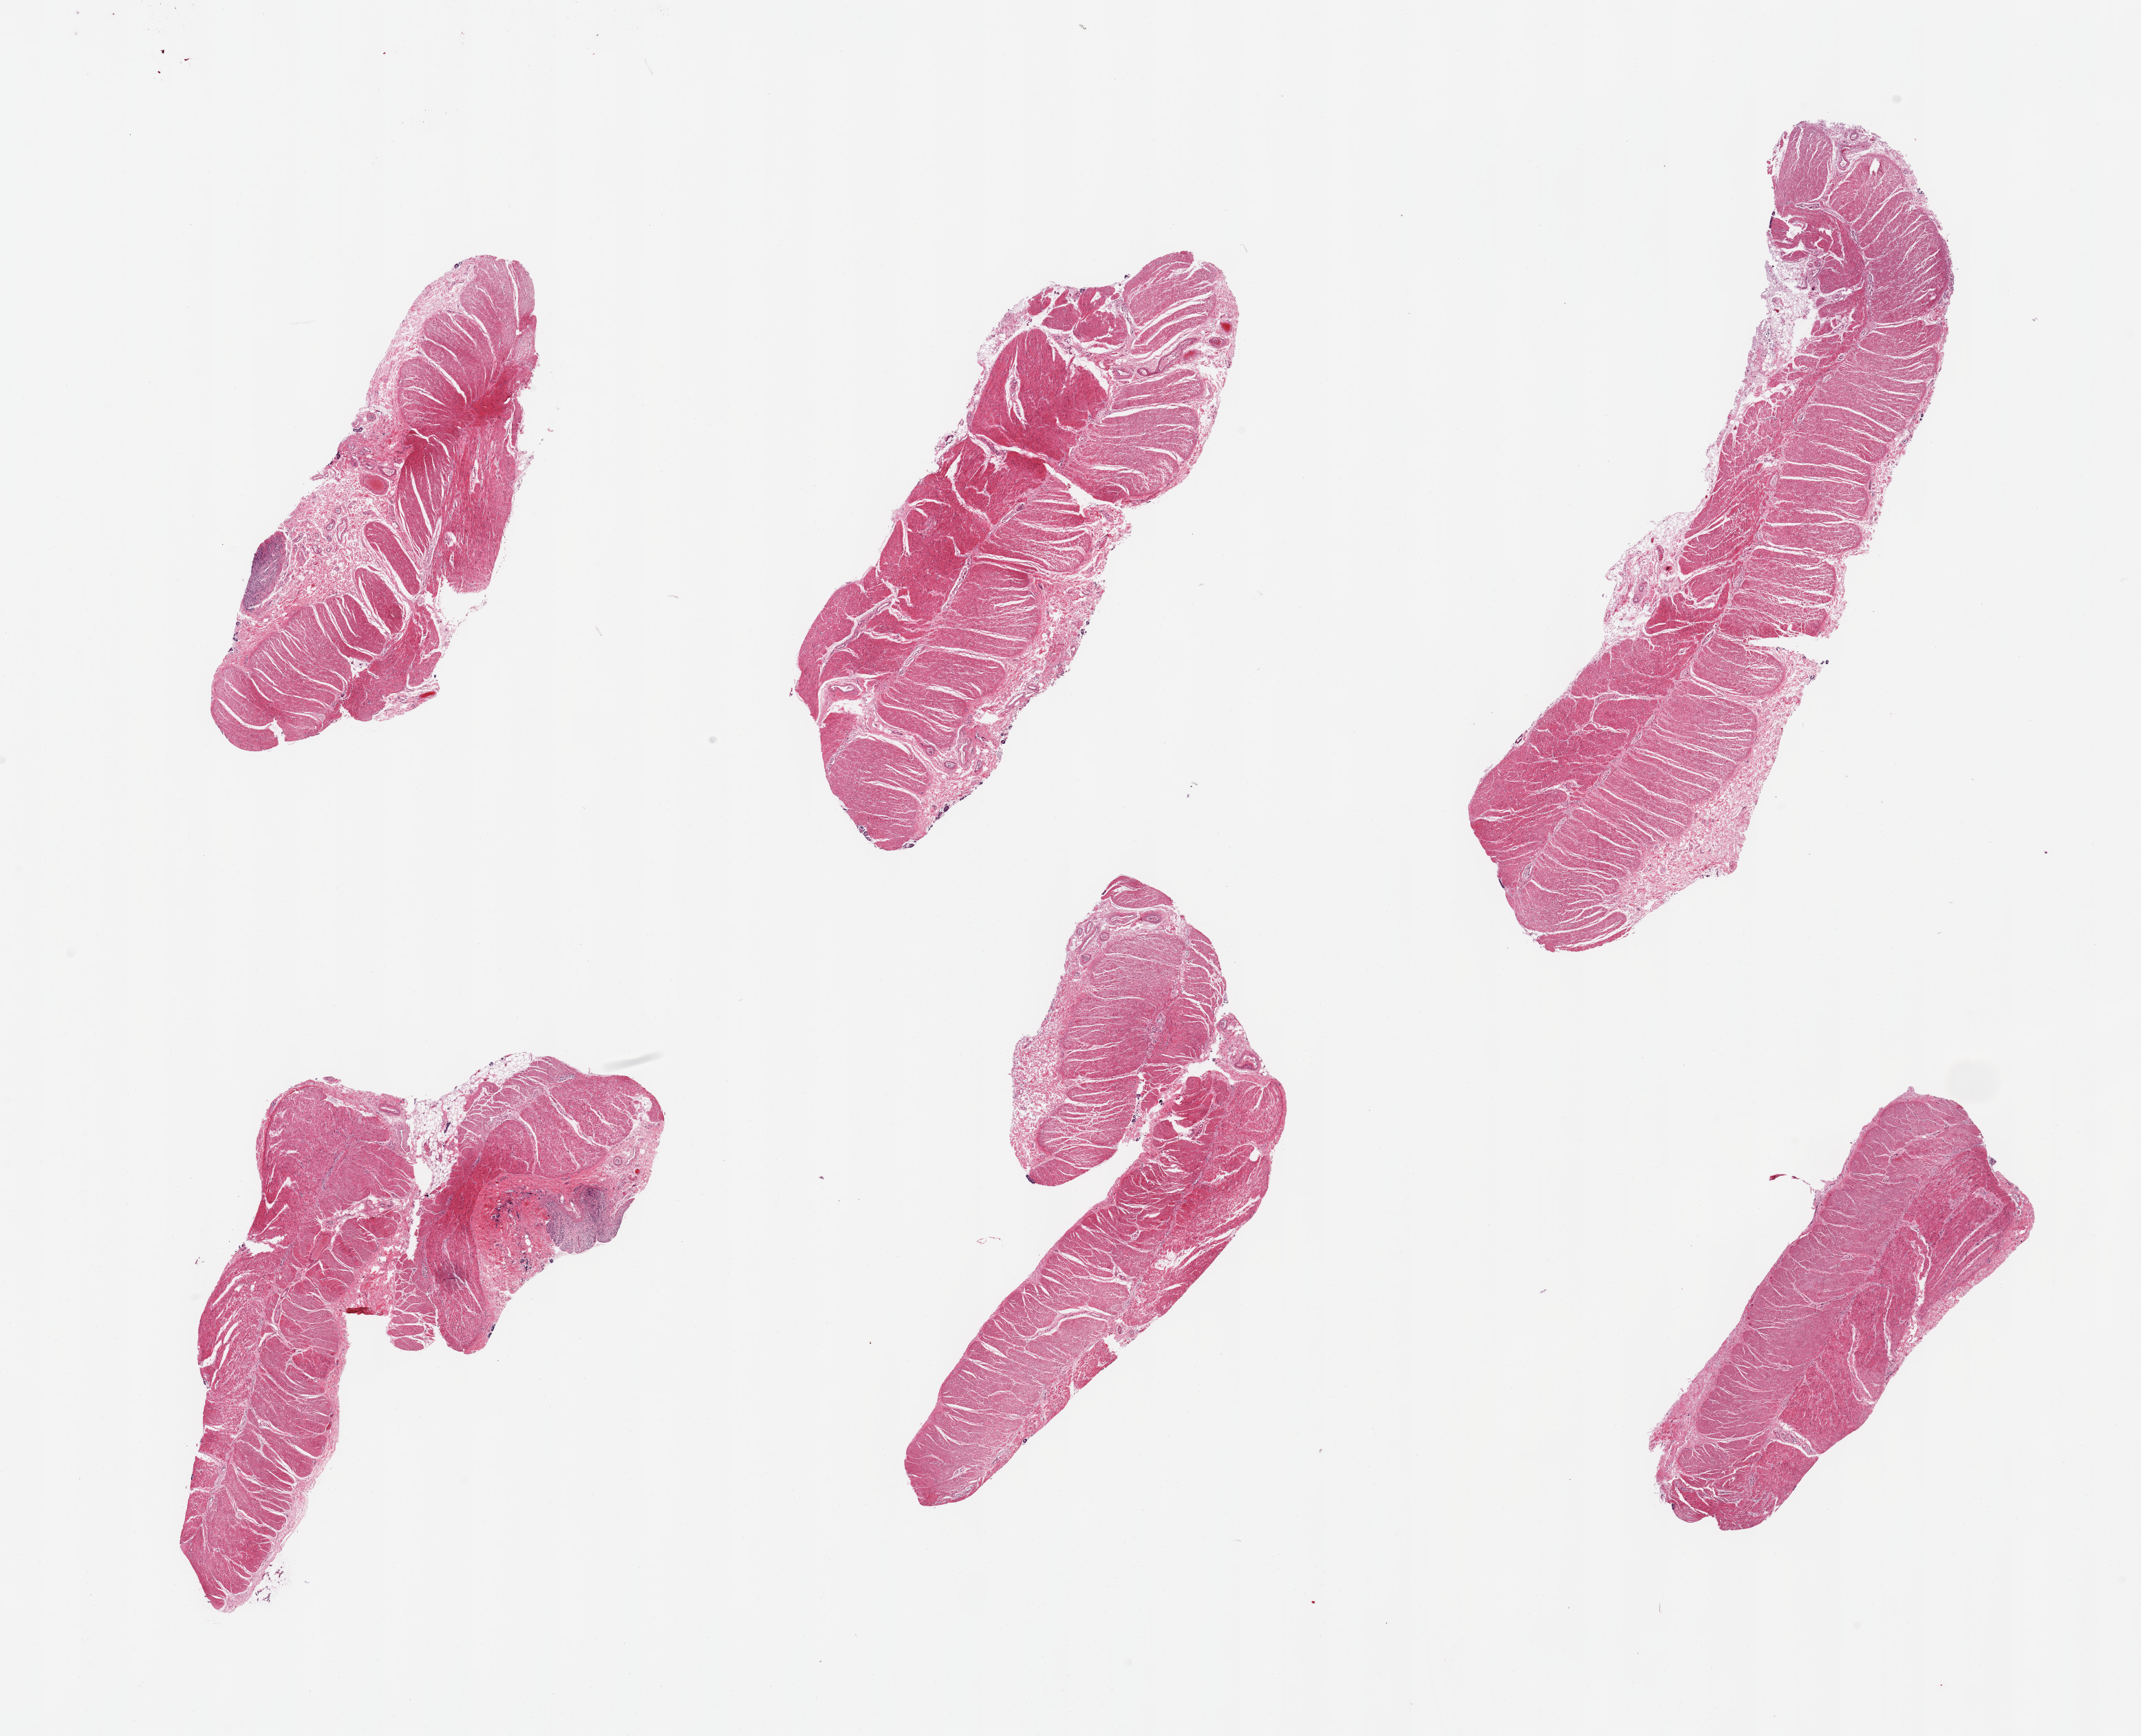
Digitized hematoxylin and eosin (H&E)-stained section, a low-resolution overview of the entire scanned area, about 24.6 x 20.0 mm, PAXgene-fixed, paraffin-embedded tissue, section of sigmoid colon (target tissue), tissue donor sample. Female donor.
Reviewer comment on this tissue sample: 6 pieces, confirmed target muscularis.